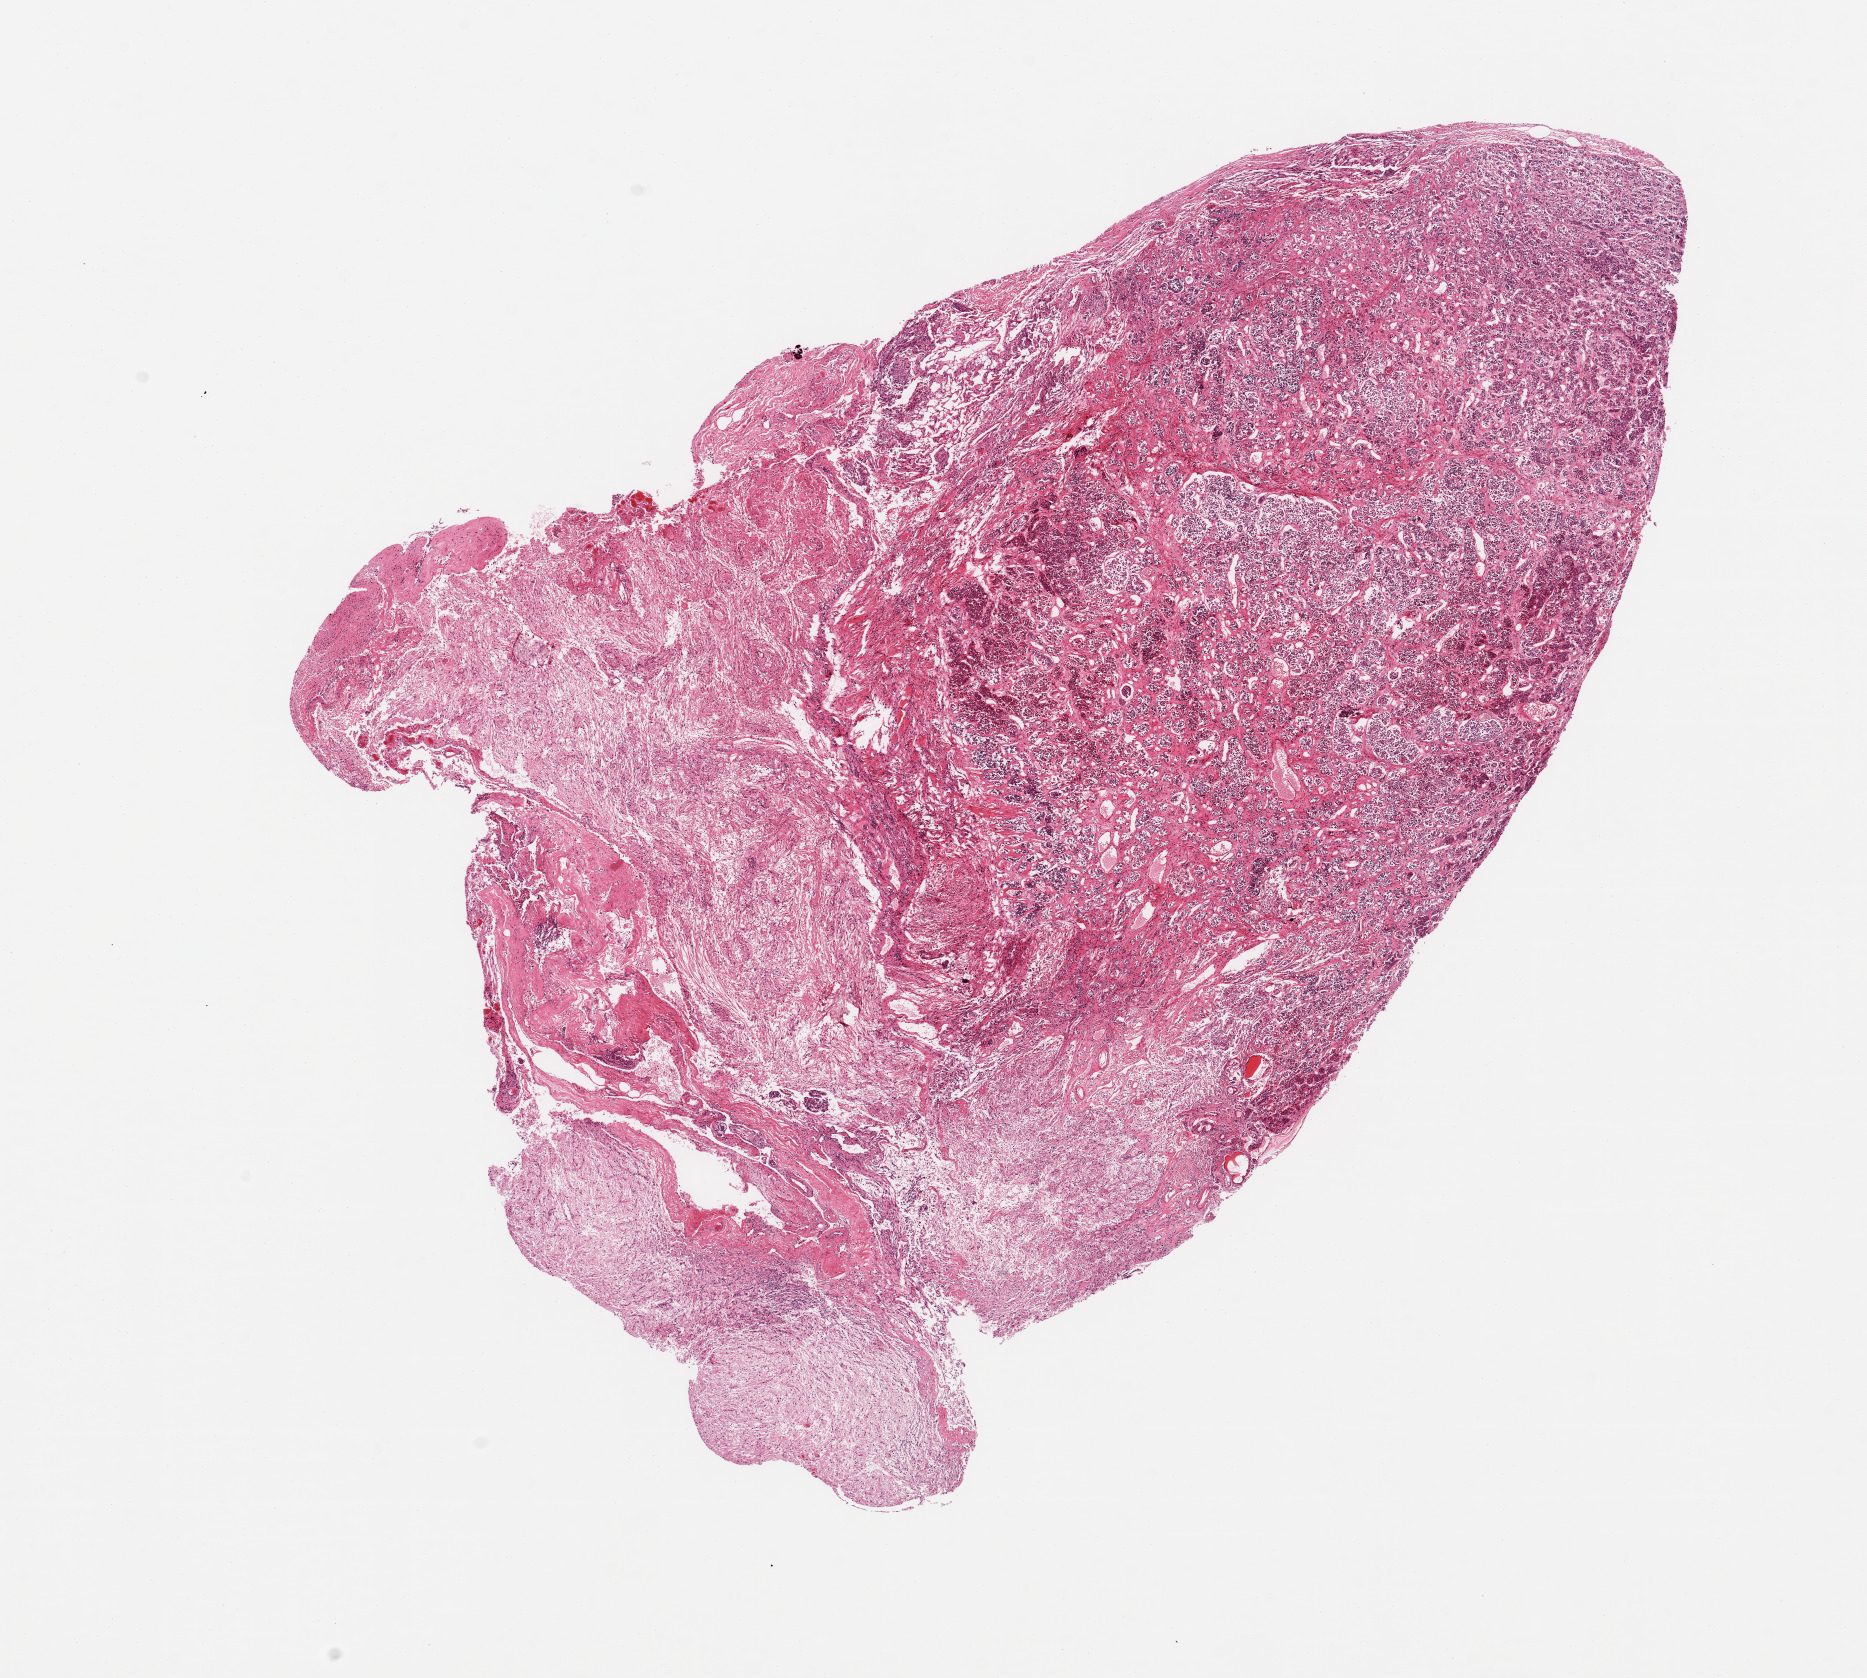
Whole-slide image, hematoxylin and eosin (H&E) stain, low-resolution overview of the scanned area, about 14.8 x 13.3 mm. PAXgene-fixed paraffin-embedded (PFPE) section. Section of pituitary (target tissue). Tissue donor sample. Donor sex: female.
* reviewer comment on this tissue sample: 1 piece, ~40% neurohypophysis; rest moderatey autolyzed adenohypophysis